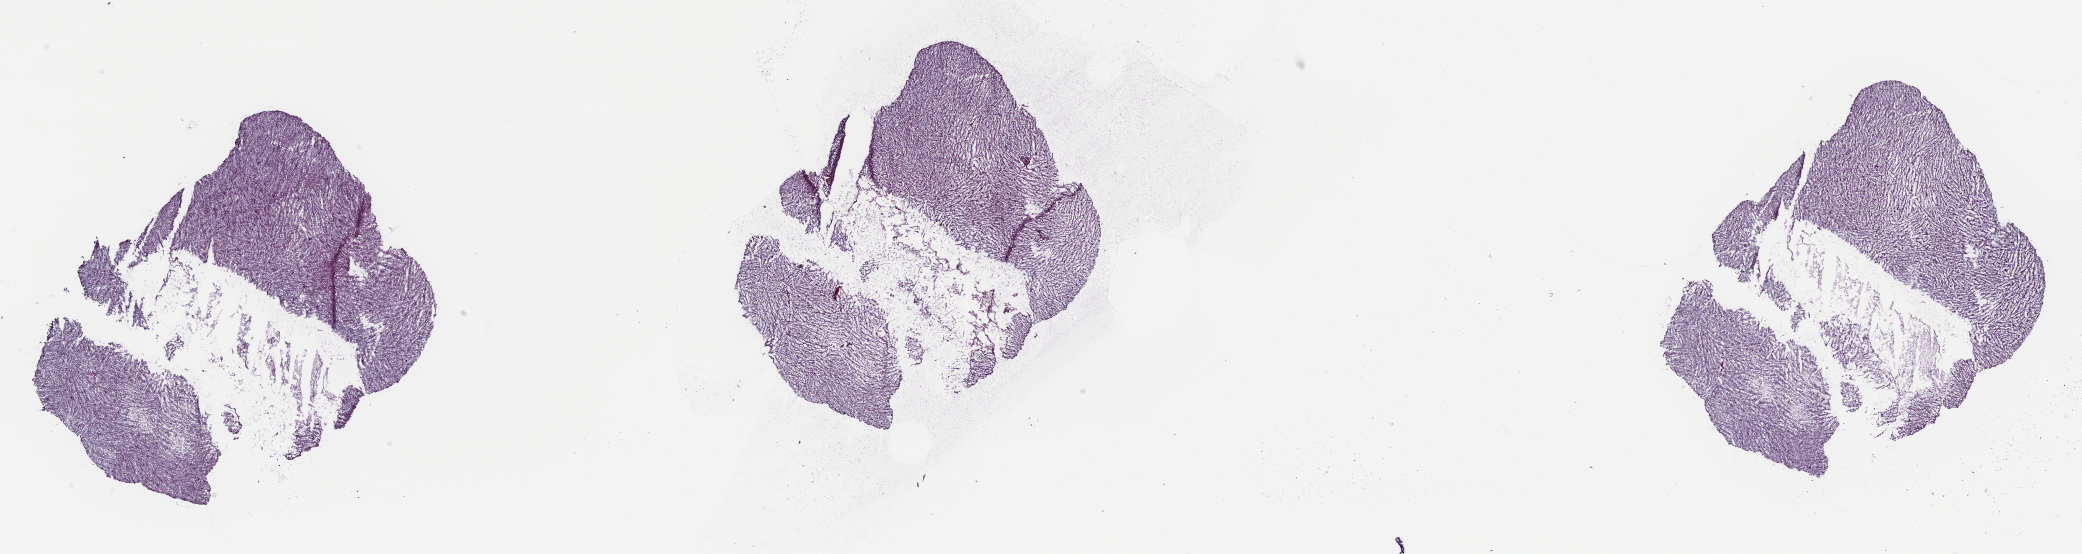
Whole-slide histology image, Hematoxylin and eosin (H&E) stained — whole scanned area (about 32.9 x 8.7 mm) shown as a low-resolution overview. Frozen section. Brain, primary tumour sample. Female patient; age at initial diagnosis 65 years.
Pathologic diagnosis: Astrocytoma, anaplastic (cerebrum).